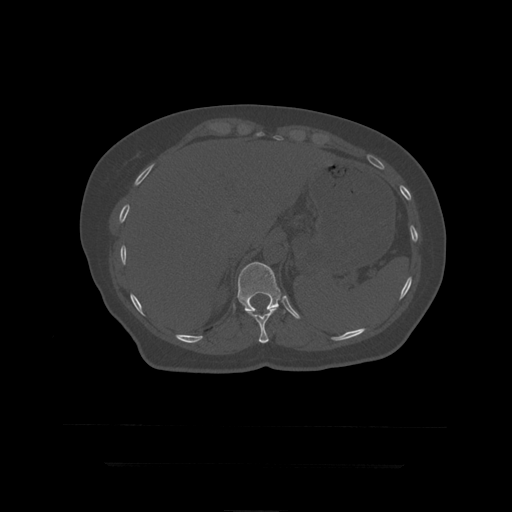
CT including the spine, one axial slice; slice 208 of 399 in the series (ordered by position); bone window (W 1800 / L 400 HU); 1.25 mm slice thickness; 512 × 512 image matrix, field of view 450 × 450 mm. Patient age 41 years. Case-level facts recorded for this patient, not image findings: primary cancer: breast.
Annotated regions visible in this slice (semi-automatic segmentation, software-assisted and operator-edited):
- T11 vertebra: box from (x=247, y=308) to (x=277, y=344) px
- T12 vertebra: (x=237, y=262)–(x=289, y=314)